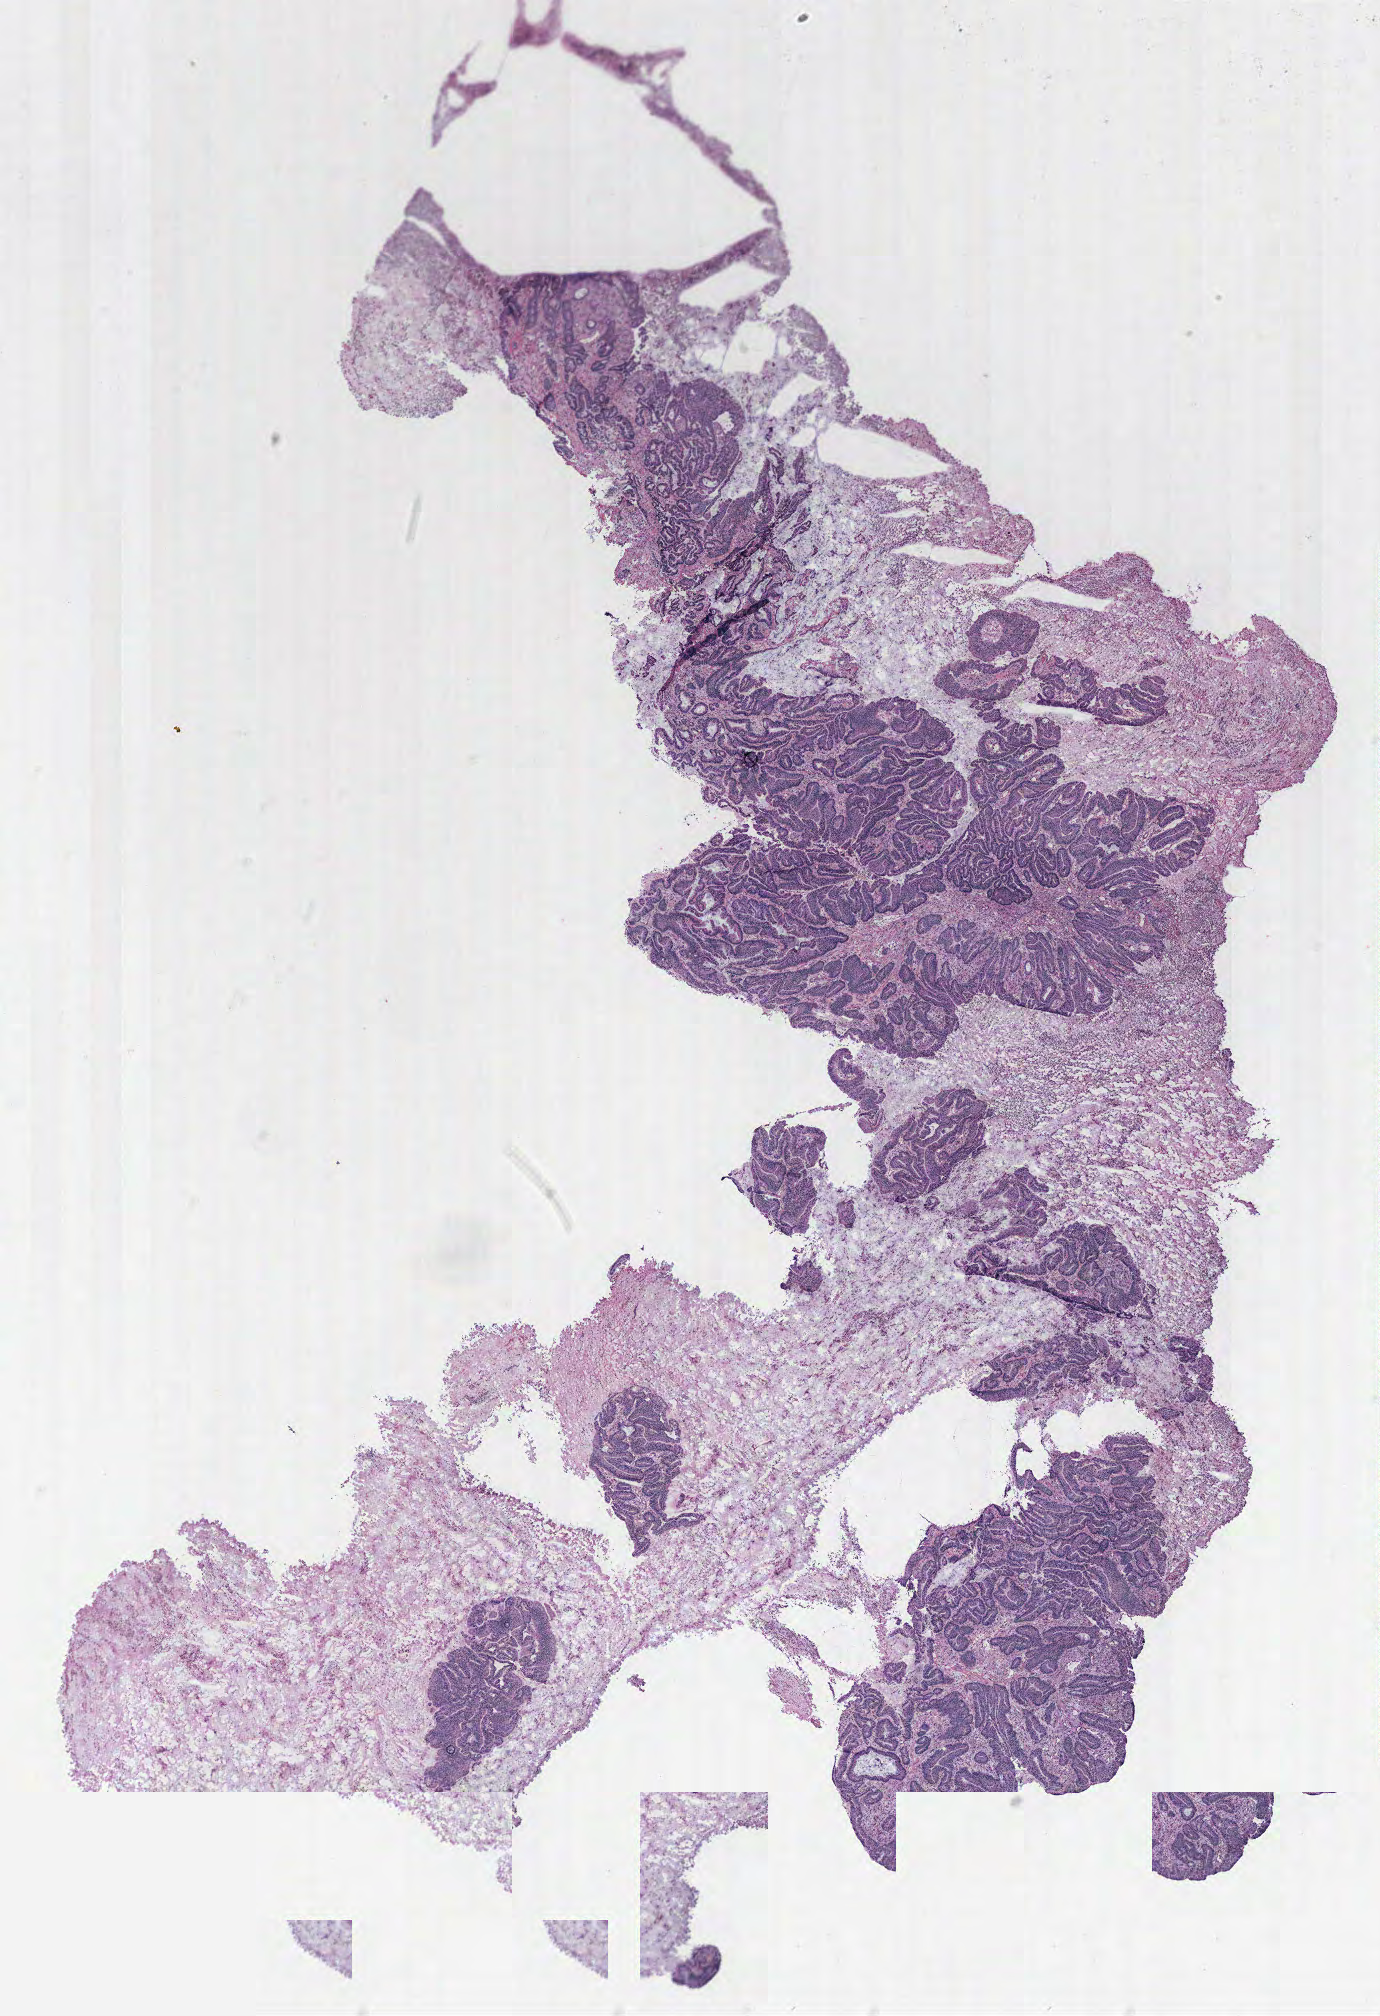
Whole-slide histology image, H&E-stained — shown as a low-resolution overview of the whole scanned area (about 11.0 x 16.1 mm, slide scanned at 40x), normal (non-tumour) tissue sample, colon. 76-year-old female patient.
This section: normal (non-tumour) tissue from the same patient. Patient diagnosis: Adenocarcinoma, NOS.